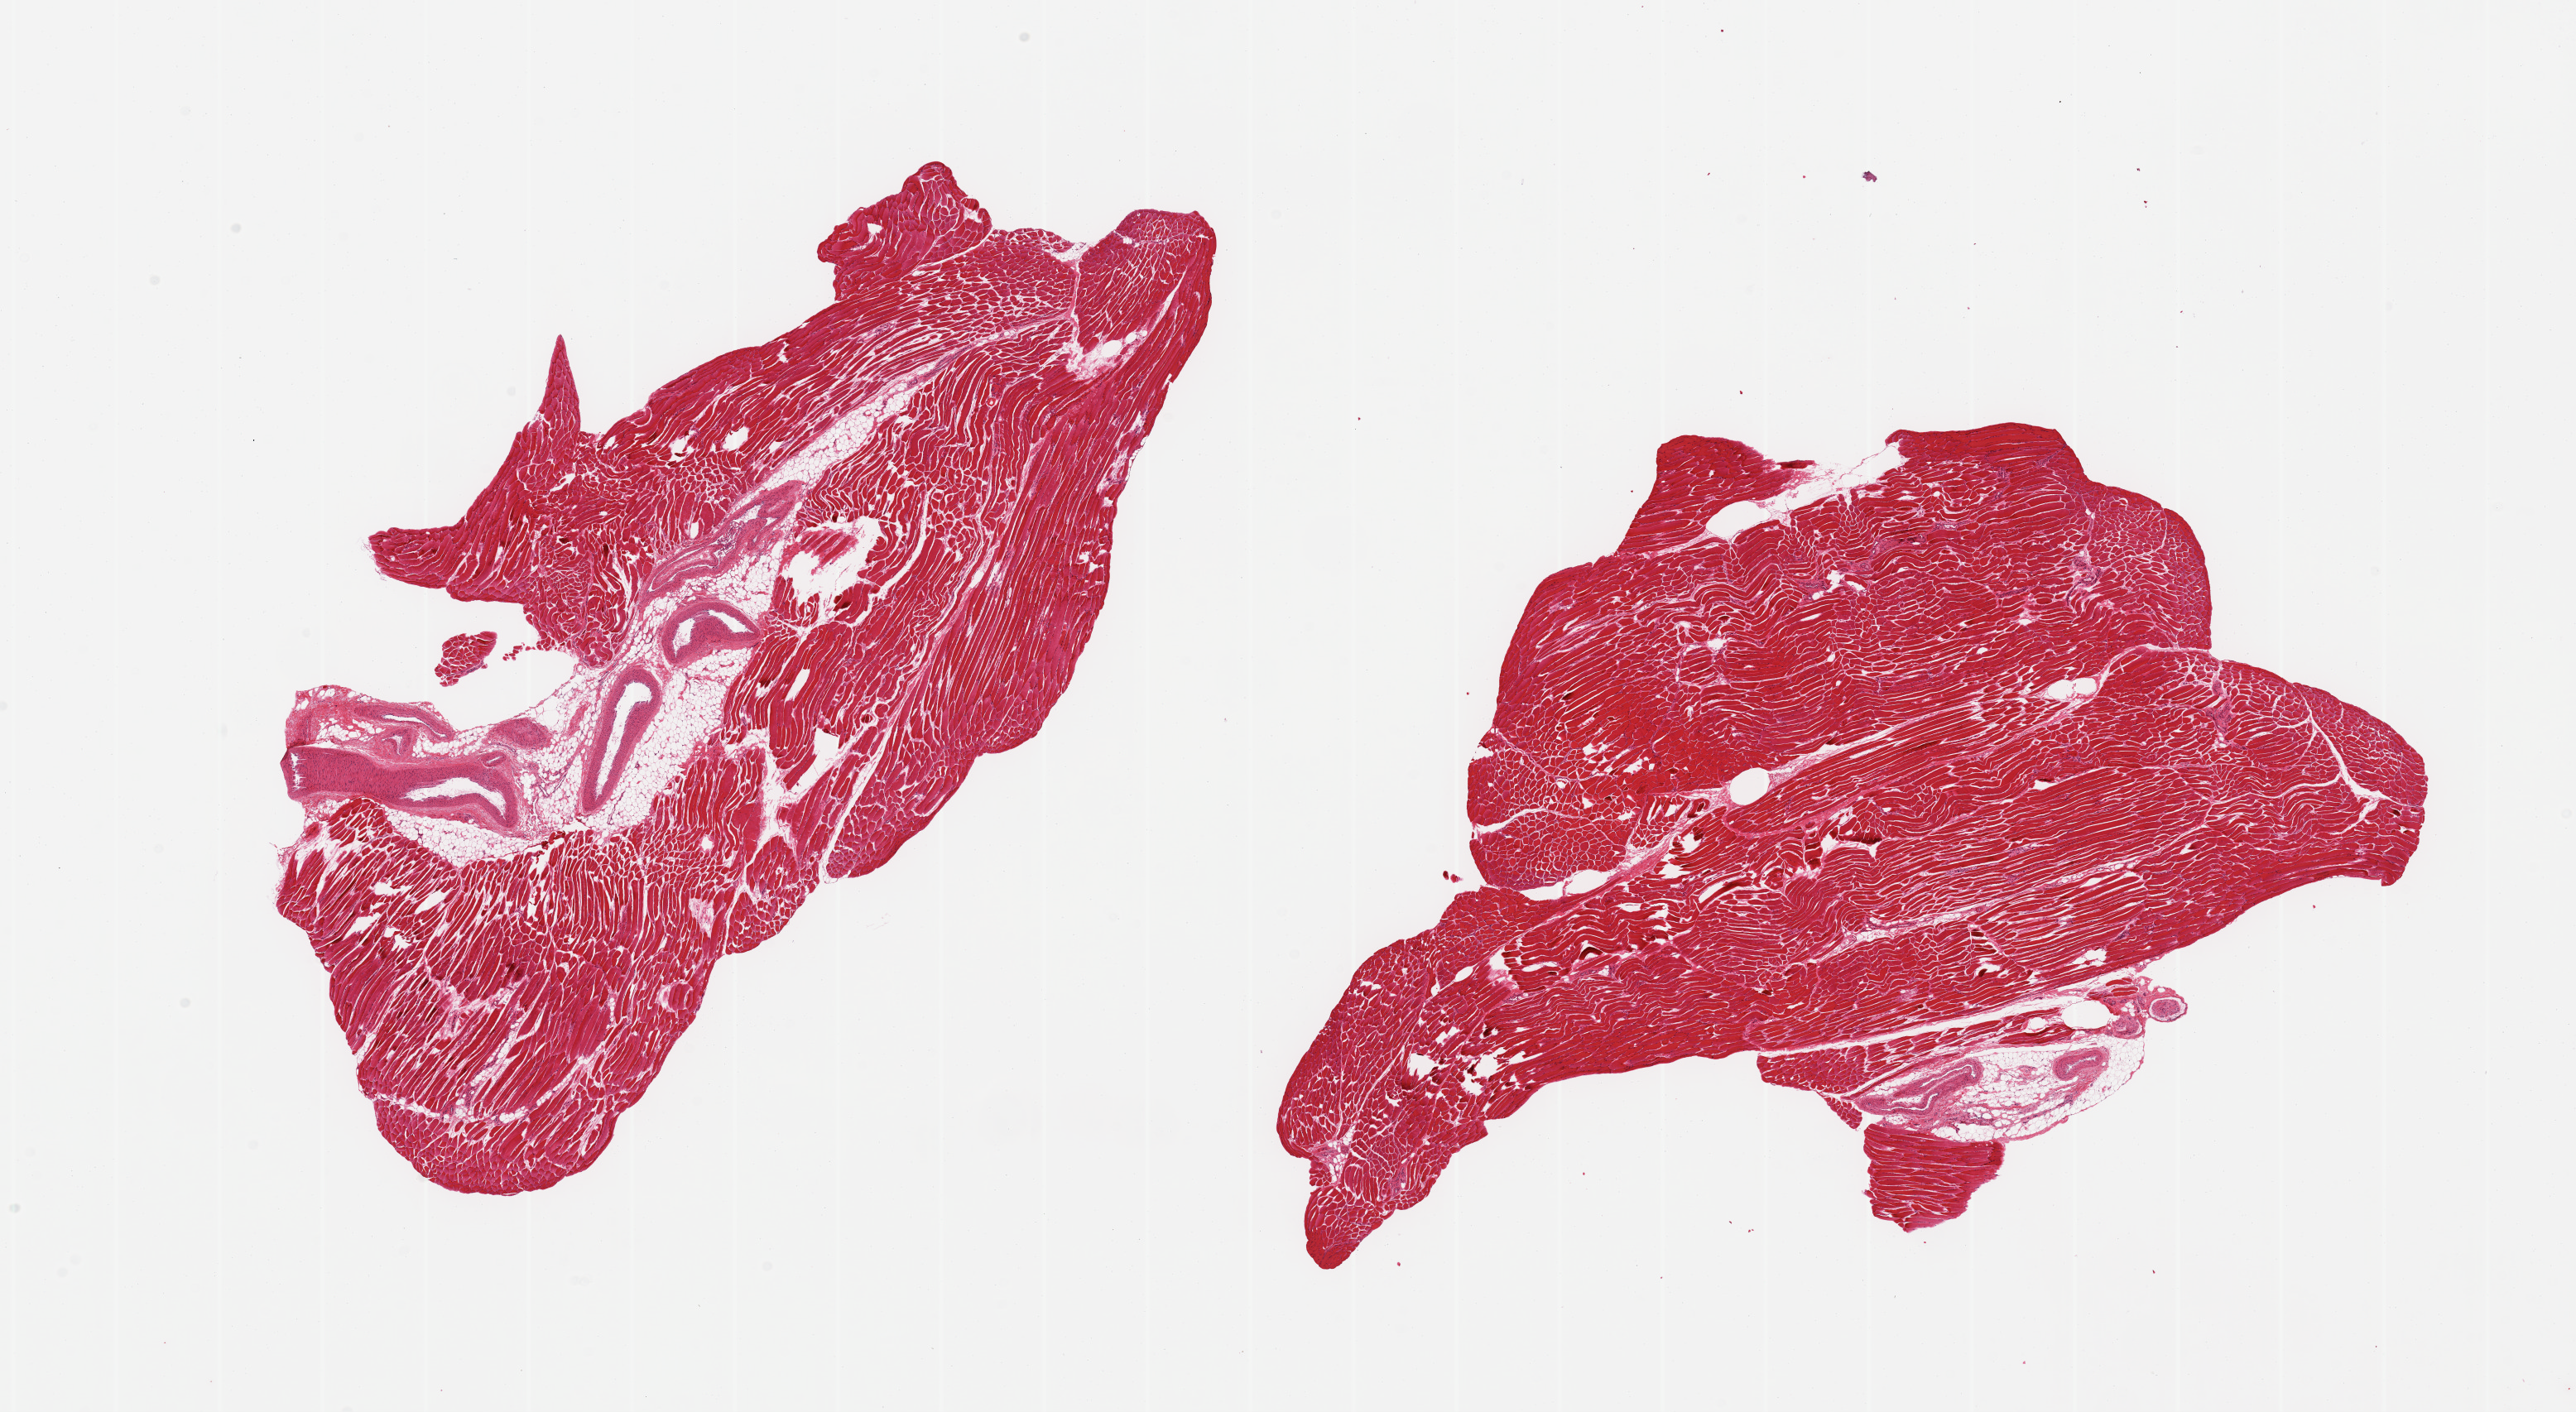
Digitized haematoxylin and eosin-stained section — whole scanned area (about 24.6 x 13.5 mm, acquisition: 20x scan) shown as a low-resolution overview, PAXgene-fixed paraffin-embedded (PFPE) section, section of skeletal muscle (target tissue), tissue donor sample. Donor sex: male.
Pathologist's review note for this sample: 2 pieces; skeletal muscle with from 5-15% fat/vessels/nerve.